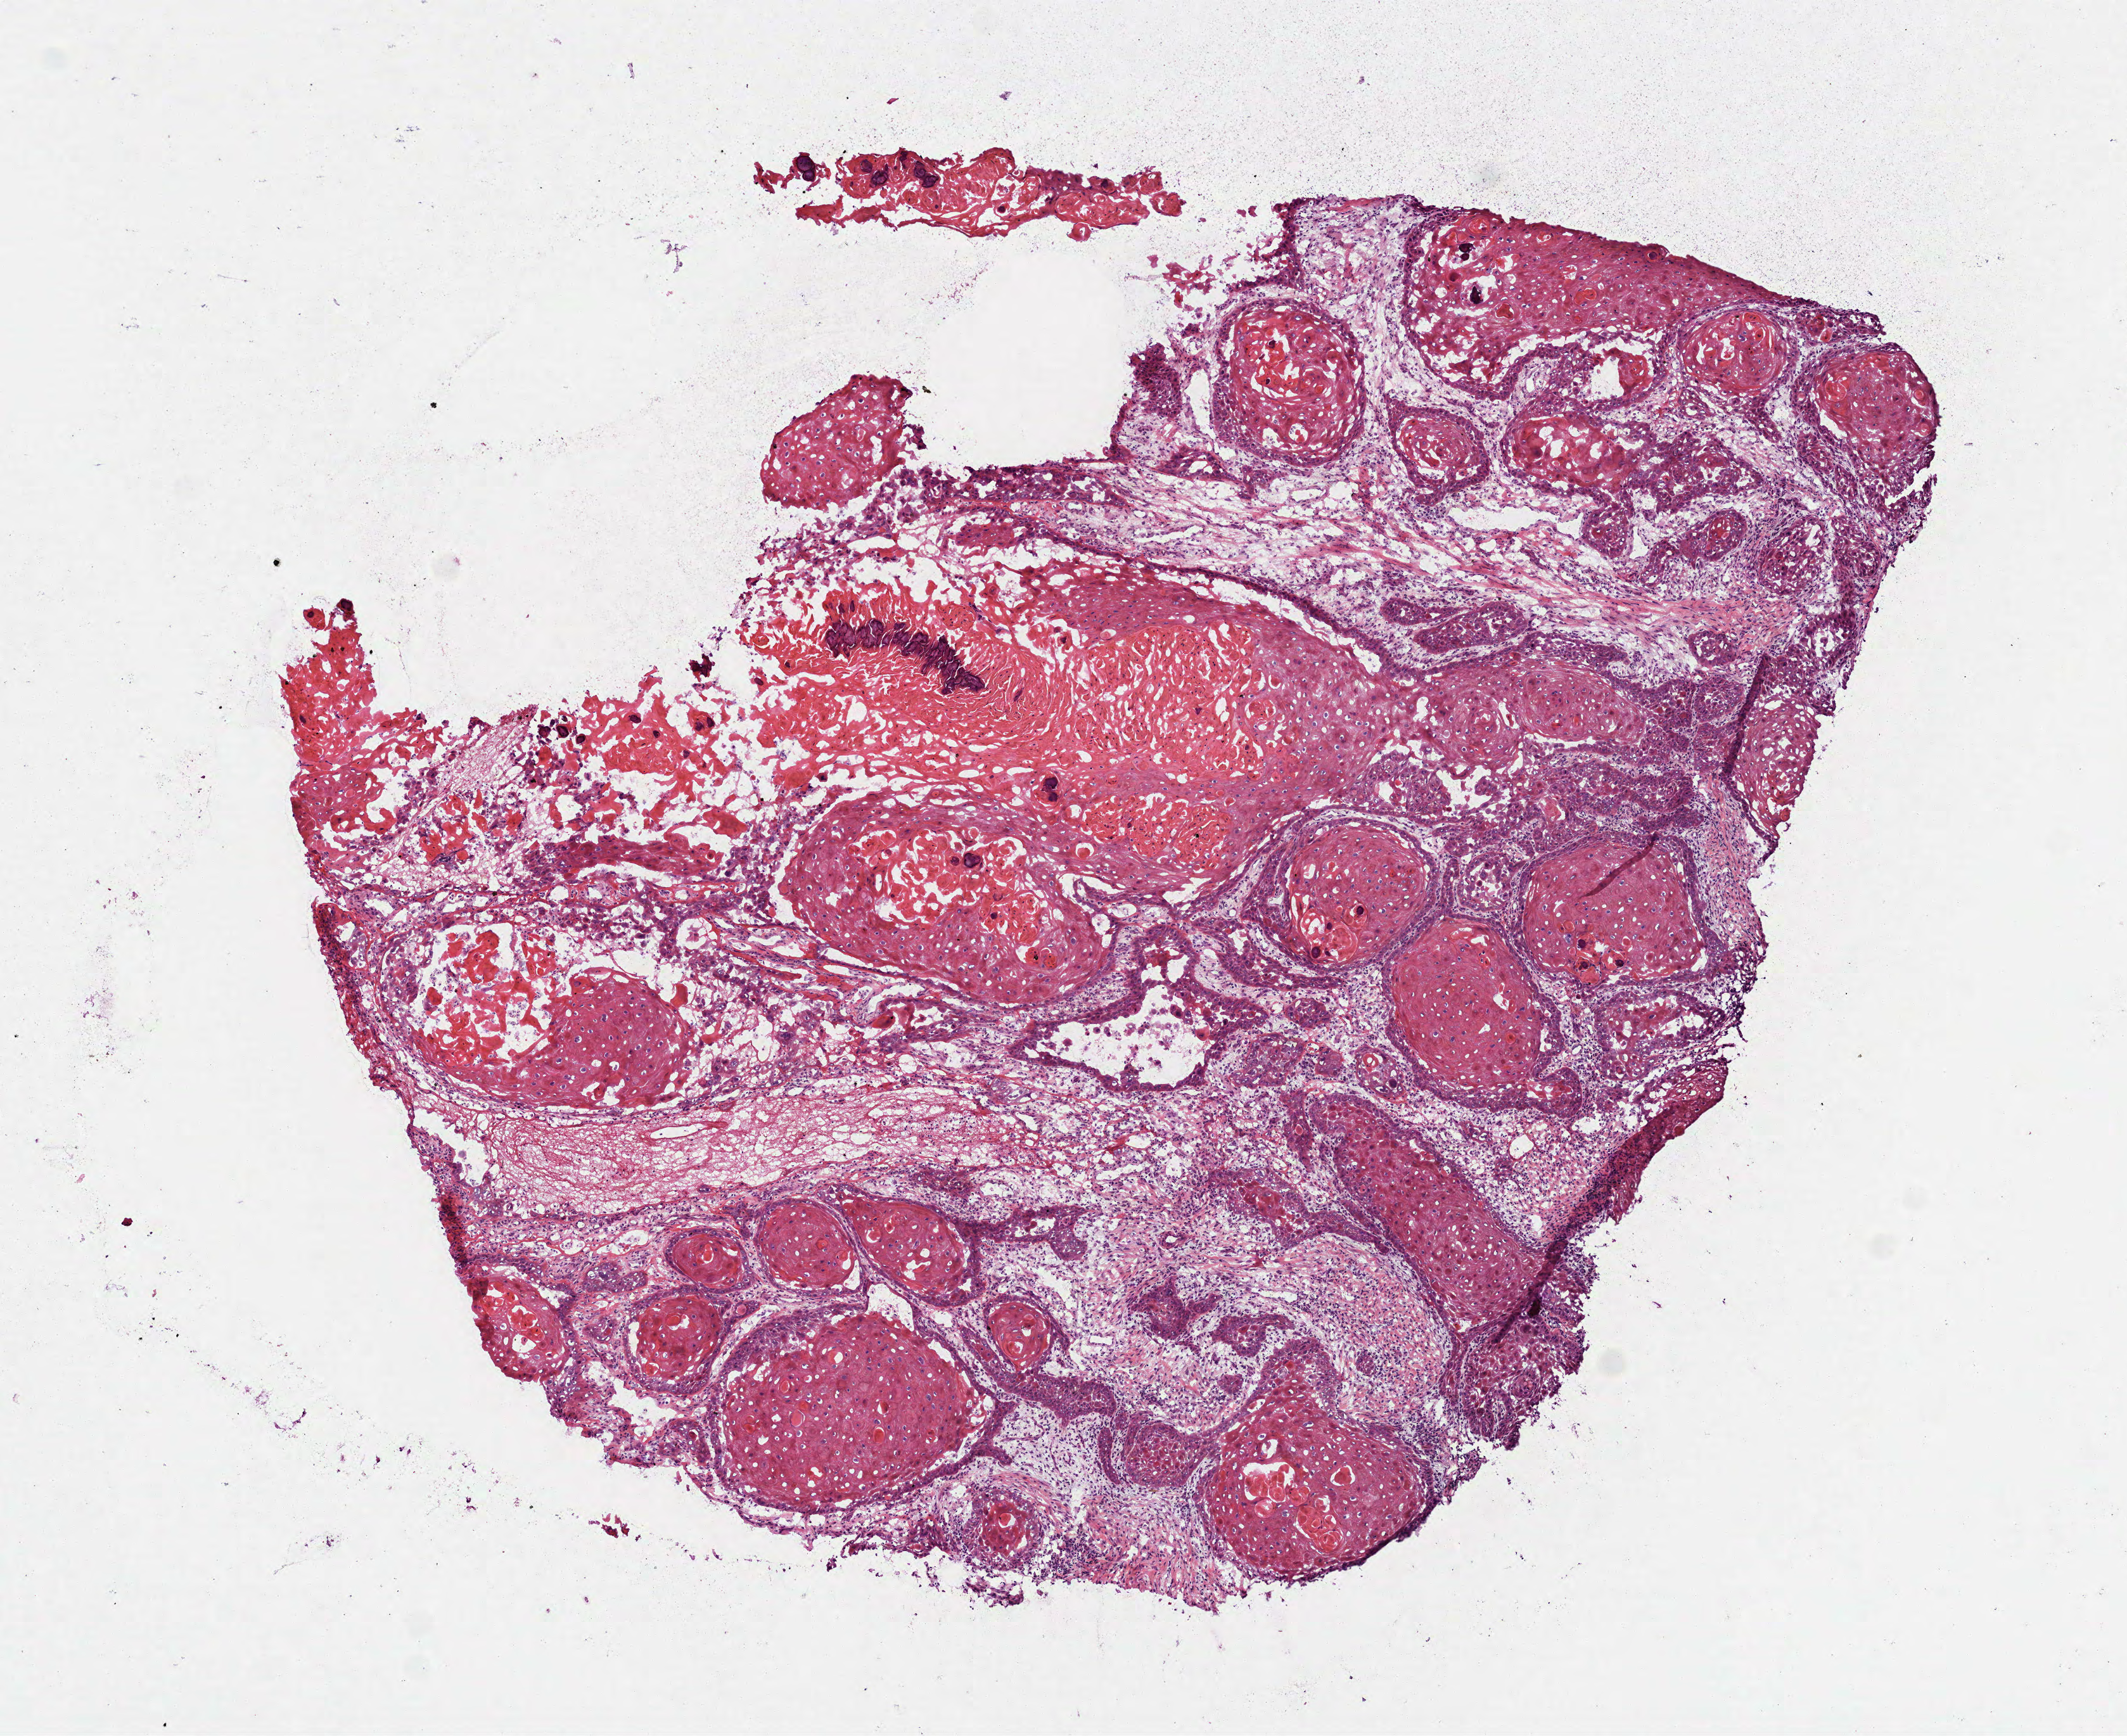
H&E whole-slide image, low-resolution overview of the scanned area, about 6.8 x 5.5 mm (slide scanned at 40x). Frozen section from the top of the tissue portion. Primary tumour sample from the head and neck. Patient: female, age at initial diagnosis 77 years. Histologic grade: G2 (moderately differentiated). Pathologist review of this section (percent, as recorded): tumour cells 70%, tumour nuclei 65%, normal cells 0%, stromal cells 28%, necrosis 2%. Inflammatory infiltration, as recorded: lymphocyte infiltration 15%.
Histologic diagnosis: Squamous cell carcinoma, NOS (mouth, NOS). AJCC pathologic stage: II (7th edition).